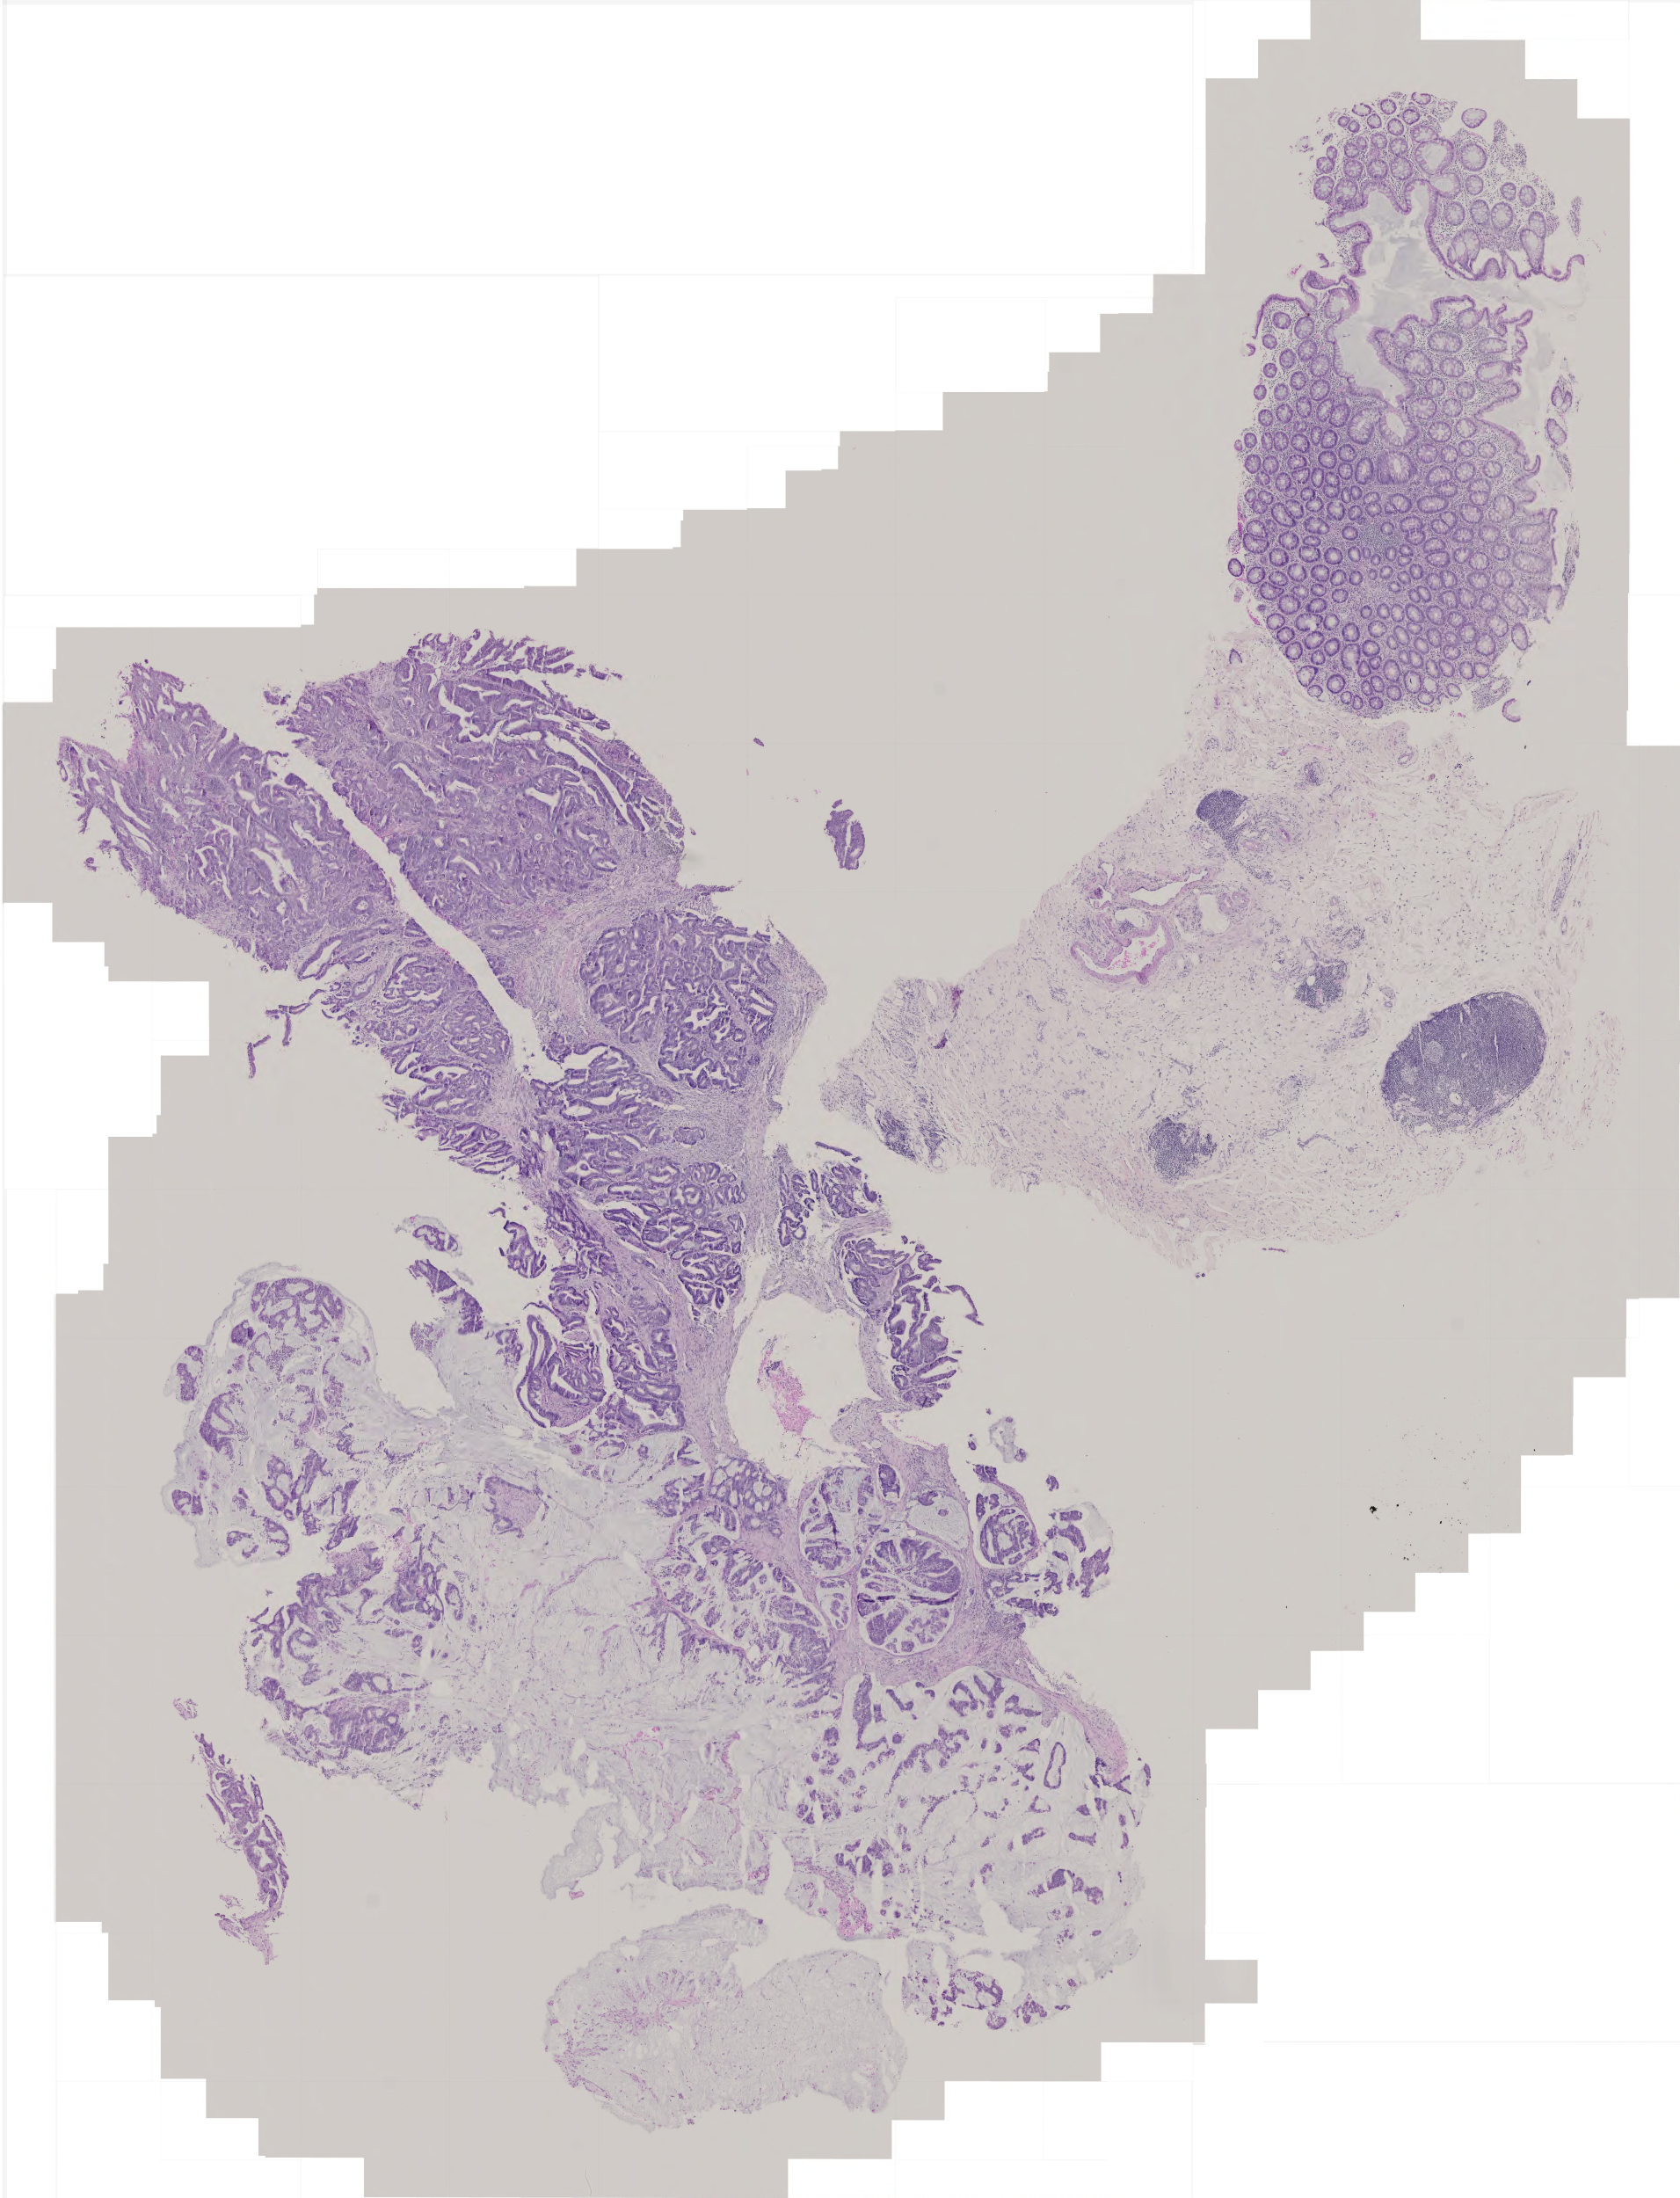
H&E-stained whole-slide image, a low-resolution overview of the entire scanned area, about 3.8 x 5.0 mm, formalin-fixed paraffin-embedded (FFPE) diagnostic section, colon, primary tumour sample. Male patient; age at initial diagnosis 68 years.
AJCC pathologic stage: IV. Lymph nodes positive (case pathology): 0 of 15 examined. Histologic diagnosis: Adenocarcinoma, NOS.